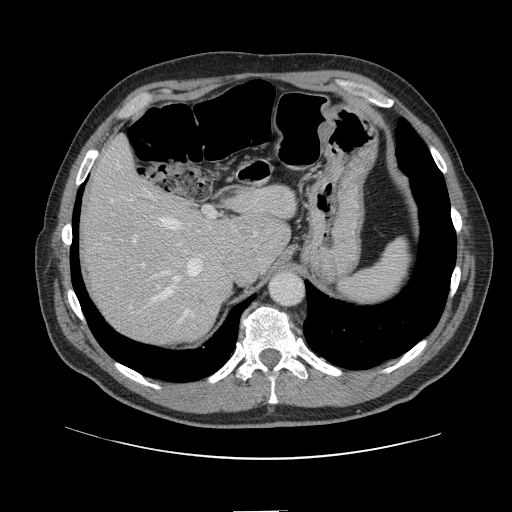
Contrast-enhanced abdominal CT, one axial slice. Position 103 of 161 along the scan axis. Intravenous contrast given. Soft-tissue window (W 400 / L 40 HU). 512 × 512 image matrix. Male patient, age 66 years. From the clinical record (not read from this slice): diagnosis: colorectal cancer liver metastases, imaged before liver resection; multiple liver metastases: no; largest metastasis: 3.5 cm; chemotherapy before resection: yes.
Annotated regions visible in this slice (expert manual segmentation):
- hepatic veins: box from (x=111, y=164) to (x=203, y=313) px
- liver: (x=83, y=142)–(x=295, y=344)
- planned liver remnant (the part of the liver to remain after resection): (x=83, y=143)–(x=295, y=308)
- portal vein (with intrahepatic branches): (x=129, y=207)–(x=216, y=309)
- liver metastasis: (x=195, y=294)–(x=208, y=308)